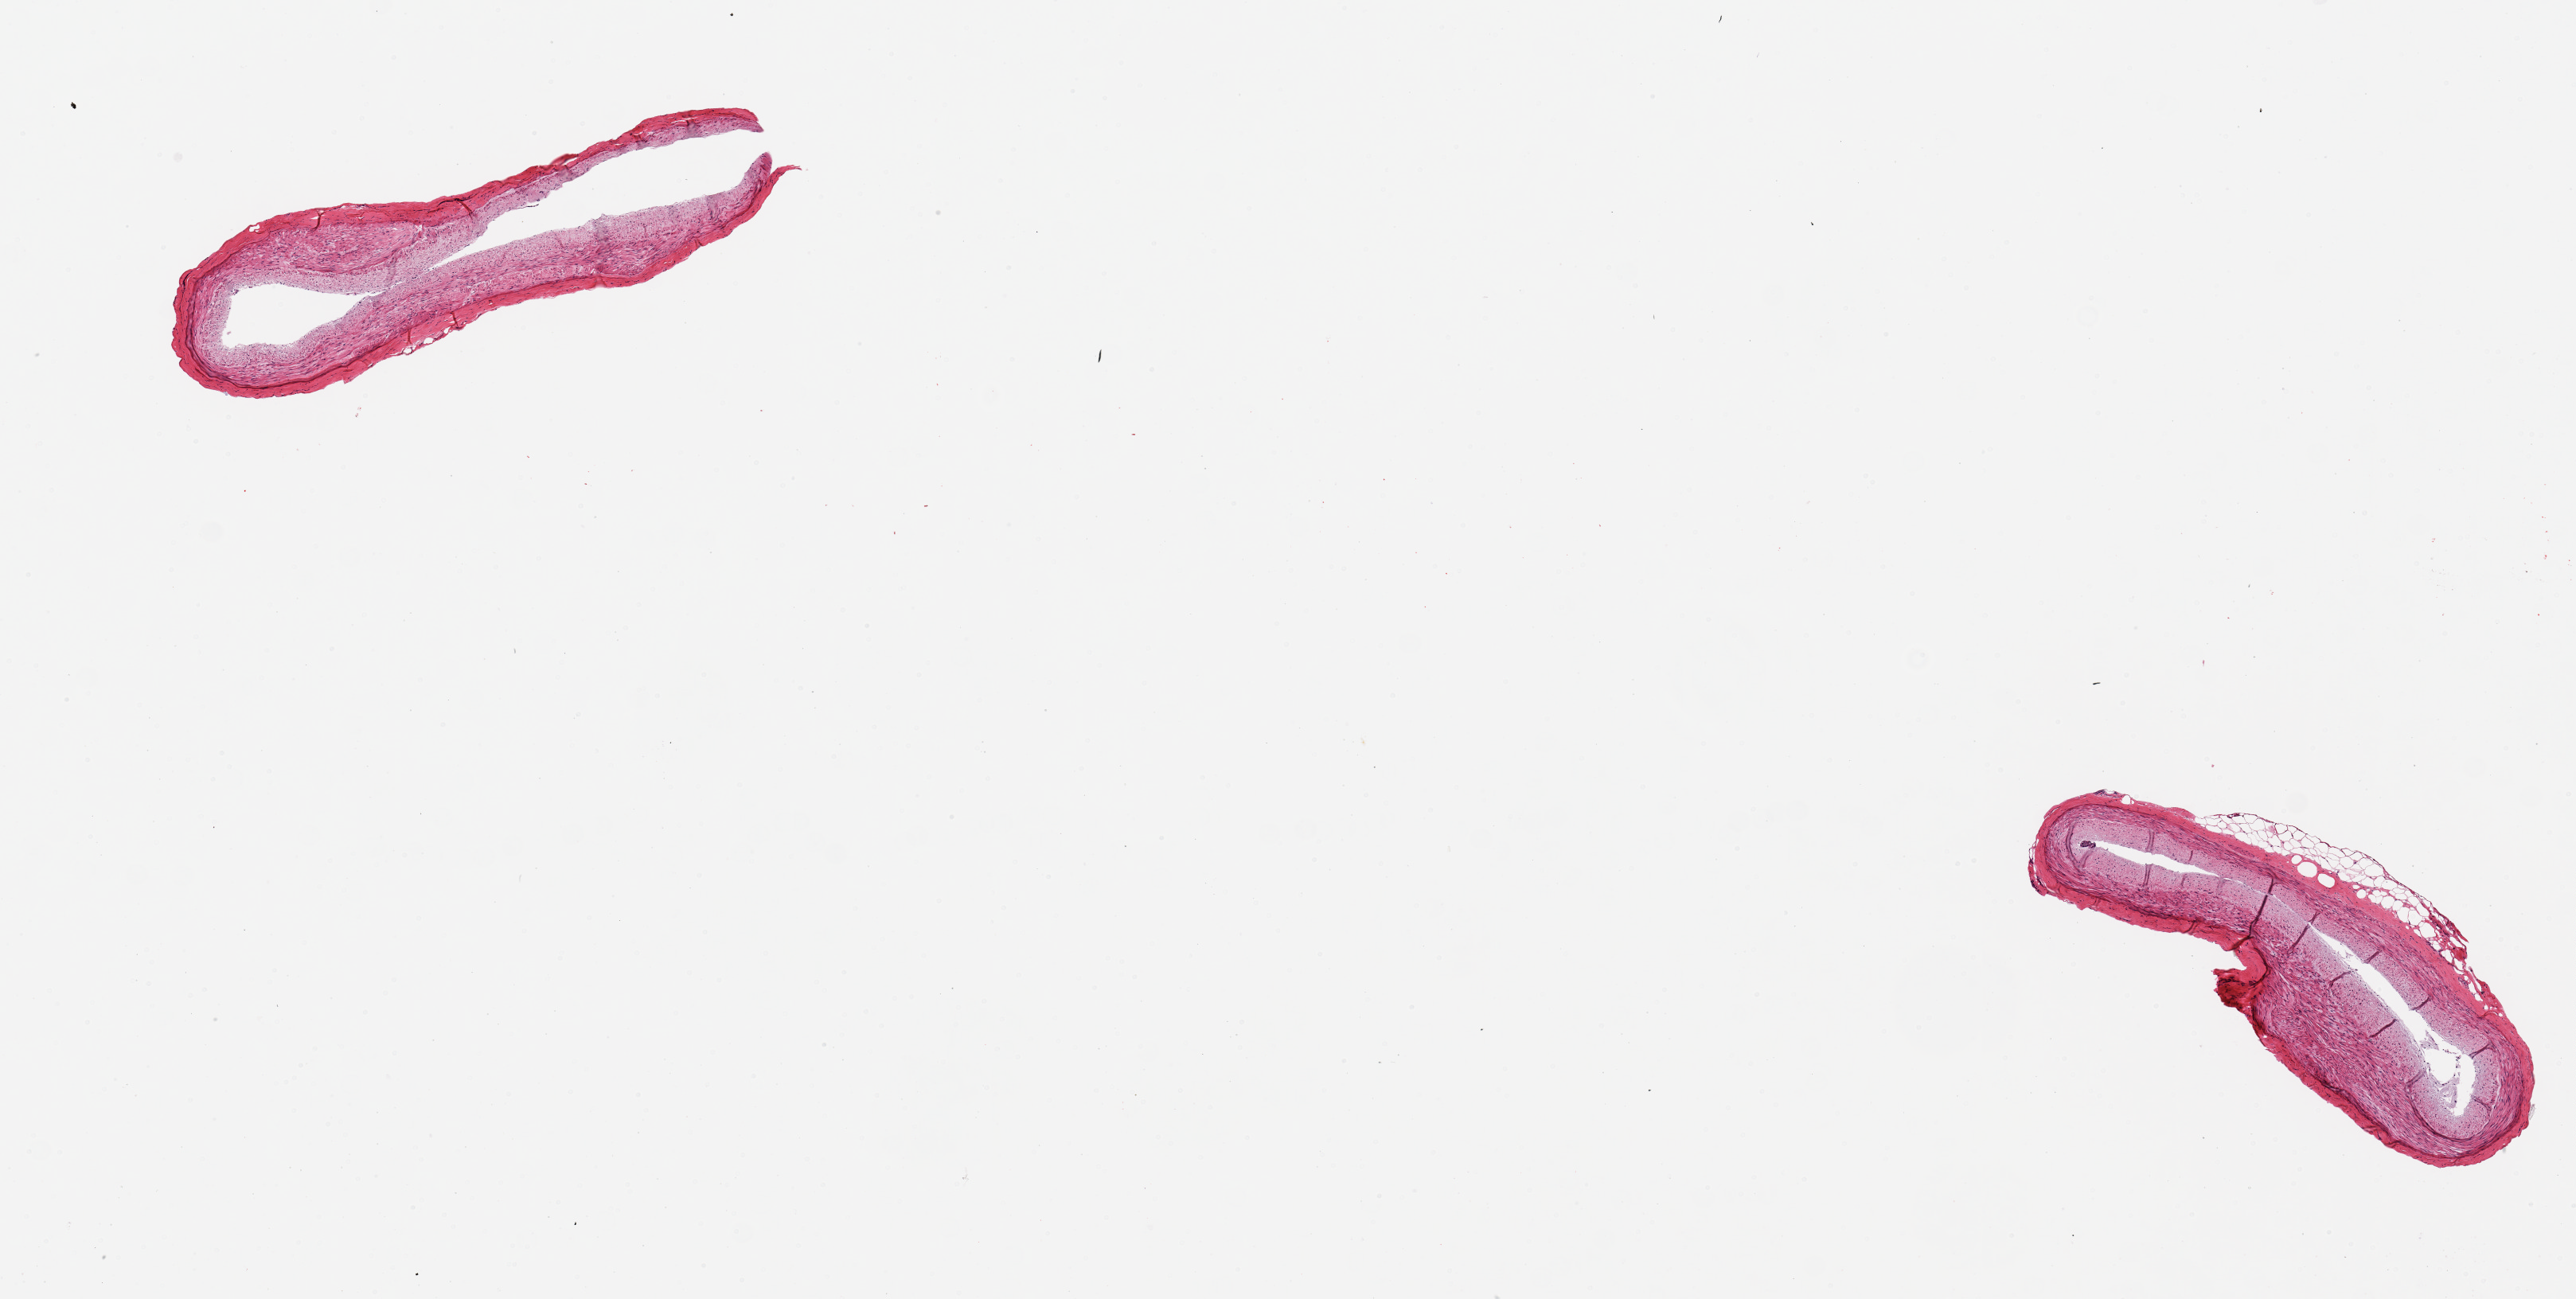
H&E whole-slide image — whole scanned area (about 12.8 x 6.5 mm, from a 20x scan) shown as a low-resolution overview, PAXgene-fixed, paraffin-embedded tissue, sampled site (target tissue): coronary artery, tissue donor sample. Donor sex: female.
Review note (as recorded): 2 pieces, 3x1mm & 3xx905um; minimal atherosclerosis.